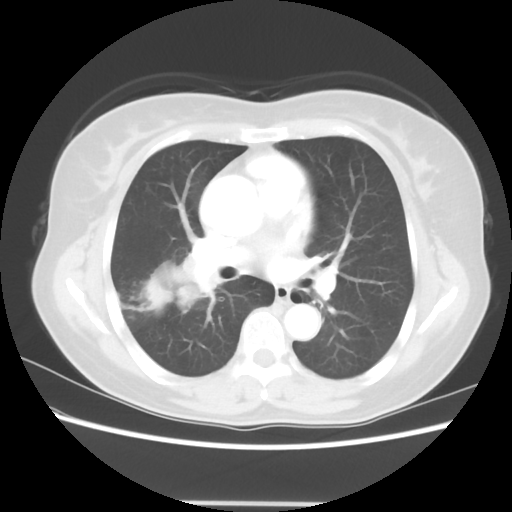
Chest CT, one axial slice. Slice 33 of 56 in the series (ordered by position). Lung window (W 1500 / L -600 HU). 512 × 512 image matrix, field of view 360 × 360 mm. Female patient, age 55 years. From the clinical record (not read from this slice): clinical TNM (as recorded): T2 N1 M0; histopathological grade: G2-3.
Annotated regions visible in this slice (bounding box drawn by a radiologist):
- lung tumour (recorded histology: adenocarcinoma): box from (x=136, y=253) to (x=213, y=332) px